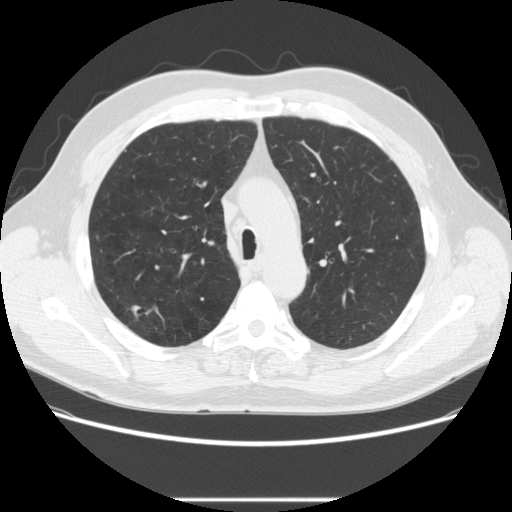
Chest CT (low-dose screening protocol), one axial image, first (baseline) screen, lung window (W 1500 / L -600 HU), 2.5 mm slice thickness, slice 75 of 270 in the series, 512 × 512 image matrix, field of view 380 × 380 mm. Male participant, aged 64 years at enrolment. Former smoker at enrolment.
• Expert reader's lesion annotation, bounding box (x1, y1, x2, y2) in pixels: (118, 298, 153, 328).
• The screening reader recorded 2 non-calcified nodules or masses ≥4 mm on this exam (right upper lobe, right upper lobe); which of them this box marks is not recorded.
• Later outcome: lung cancer diagnosed 753 days after this screen — adenocarcinoma, NOS, right upper lobe, moderately differentiated (G2), stage IA (AJCC 6th edition), 14 mm at pathology.